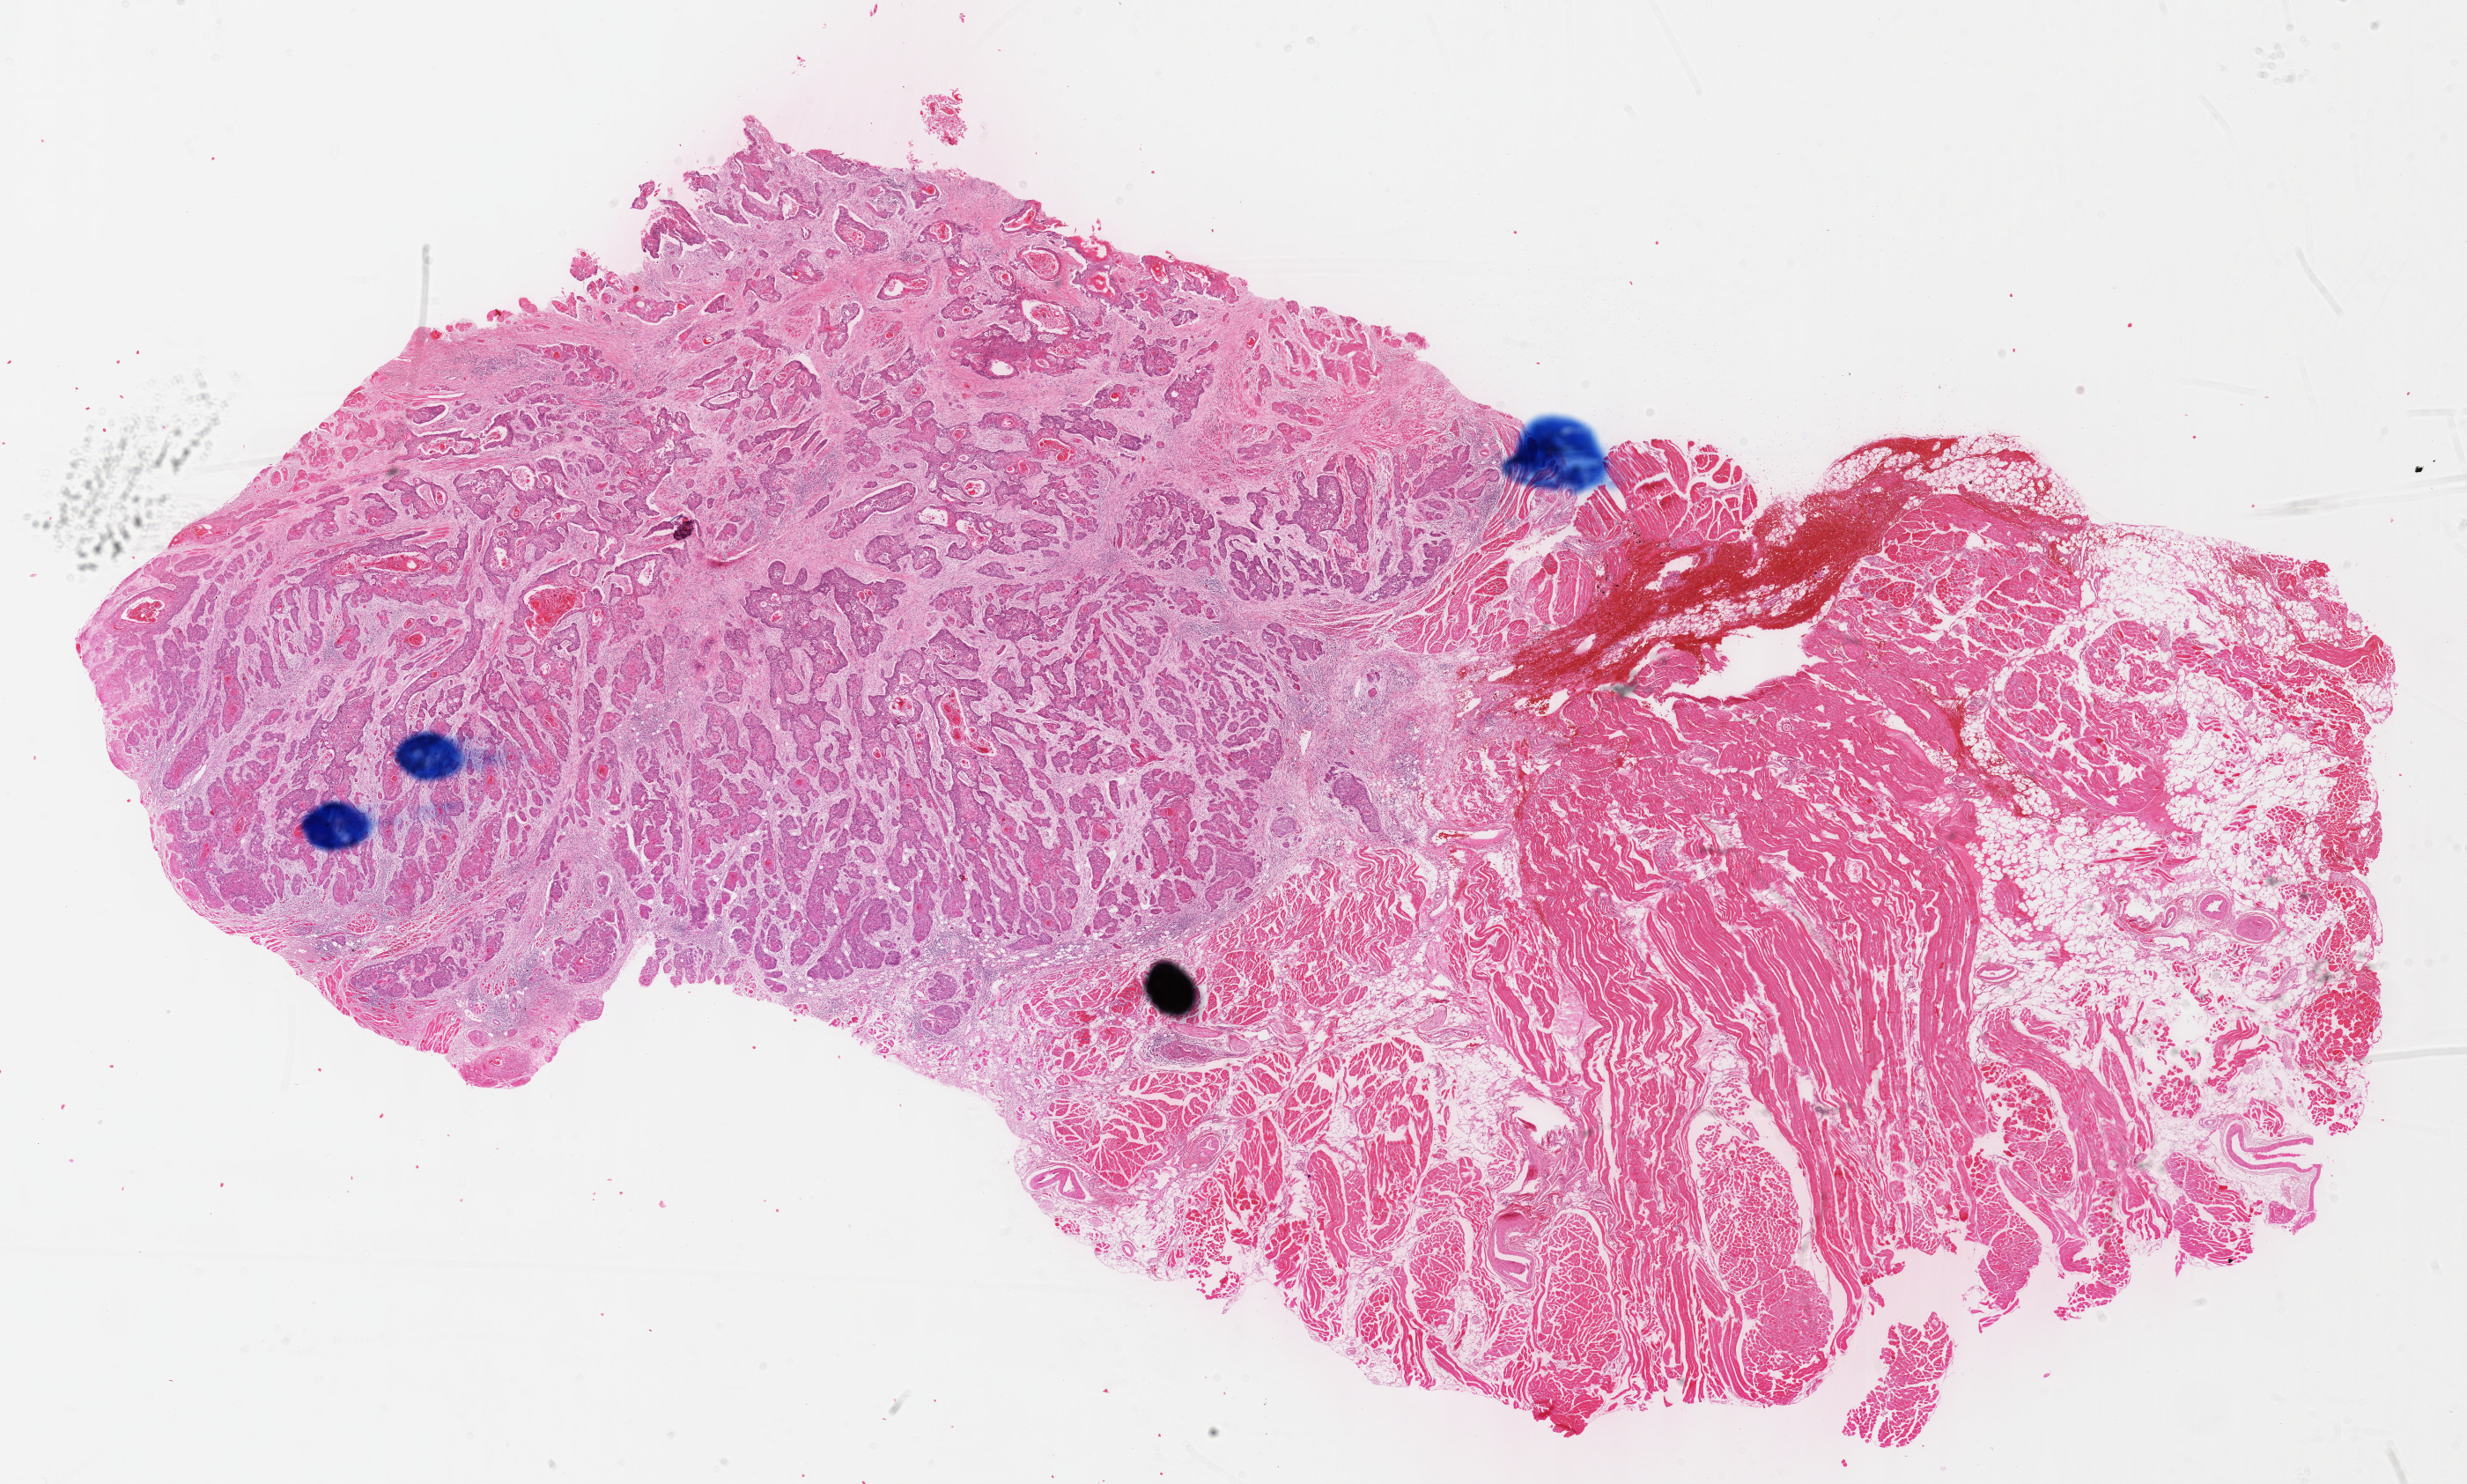
Hematoxylin and eosin (H&E) stained whole-slide image — shown as a low-resolution overview of the whole scanned area (about 22.6 x 13.6 mm, slide scanned at 40x). Formalin-fixed paraffin-embedded (FFPE) diagnostic section. Primary tumour sample from the head and neck. Male patient; age at initial diagnosis 57 years. Histologic grade: G2 (moderately differentiated).
* AJCC pathologic stage: IVA (7th edition)
* pathologic diagnosis: Squamous cell carcinoma, NOS (tongue, NOS)